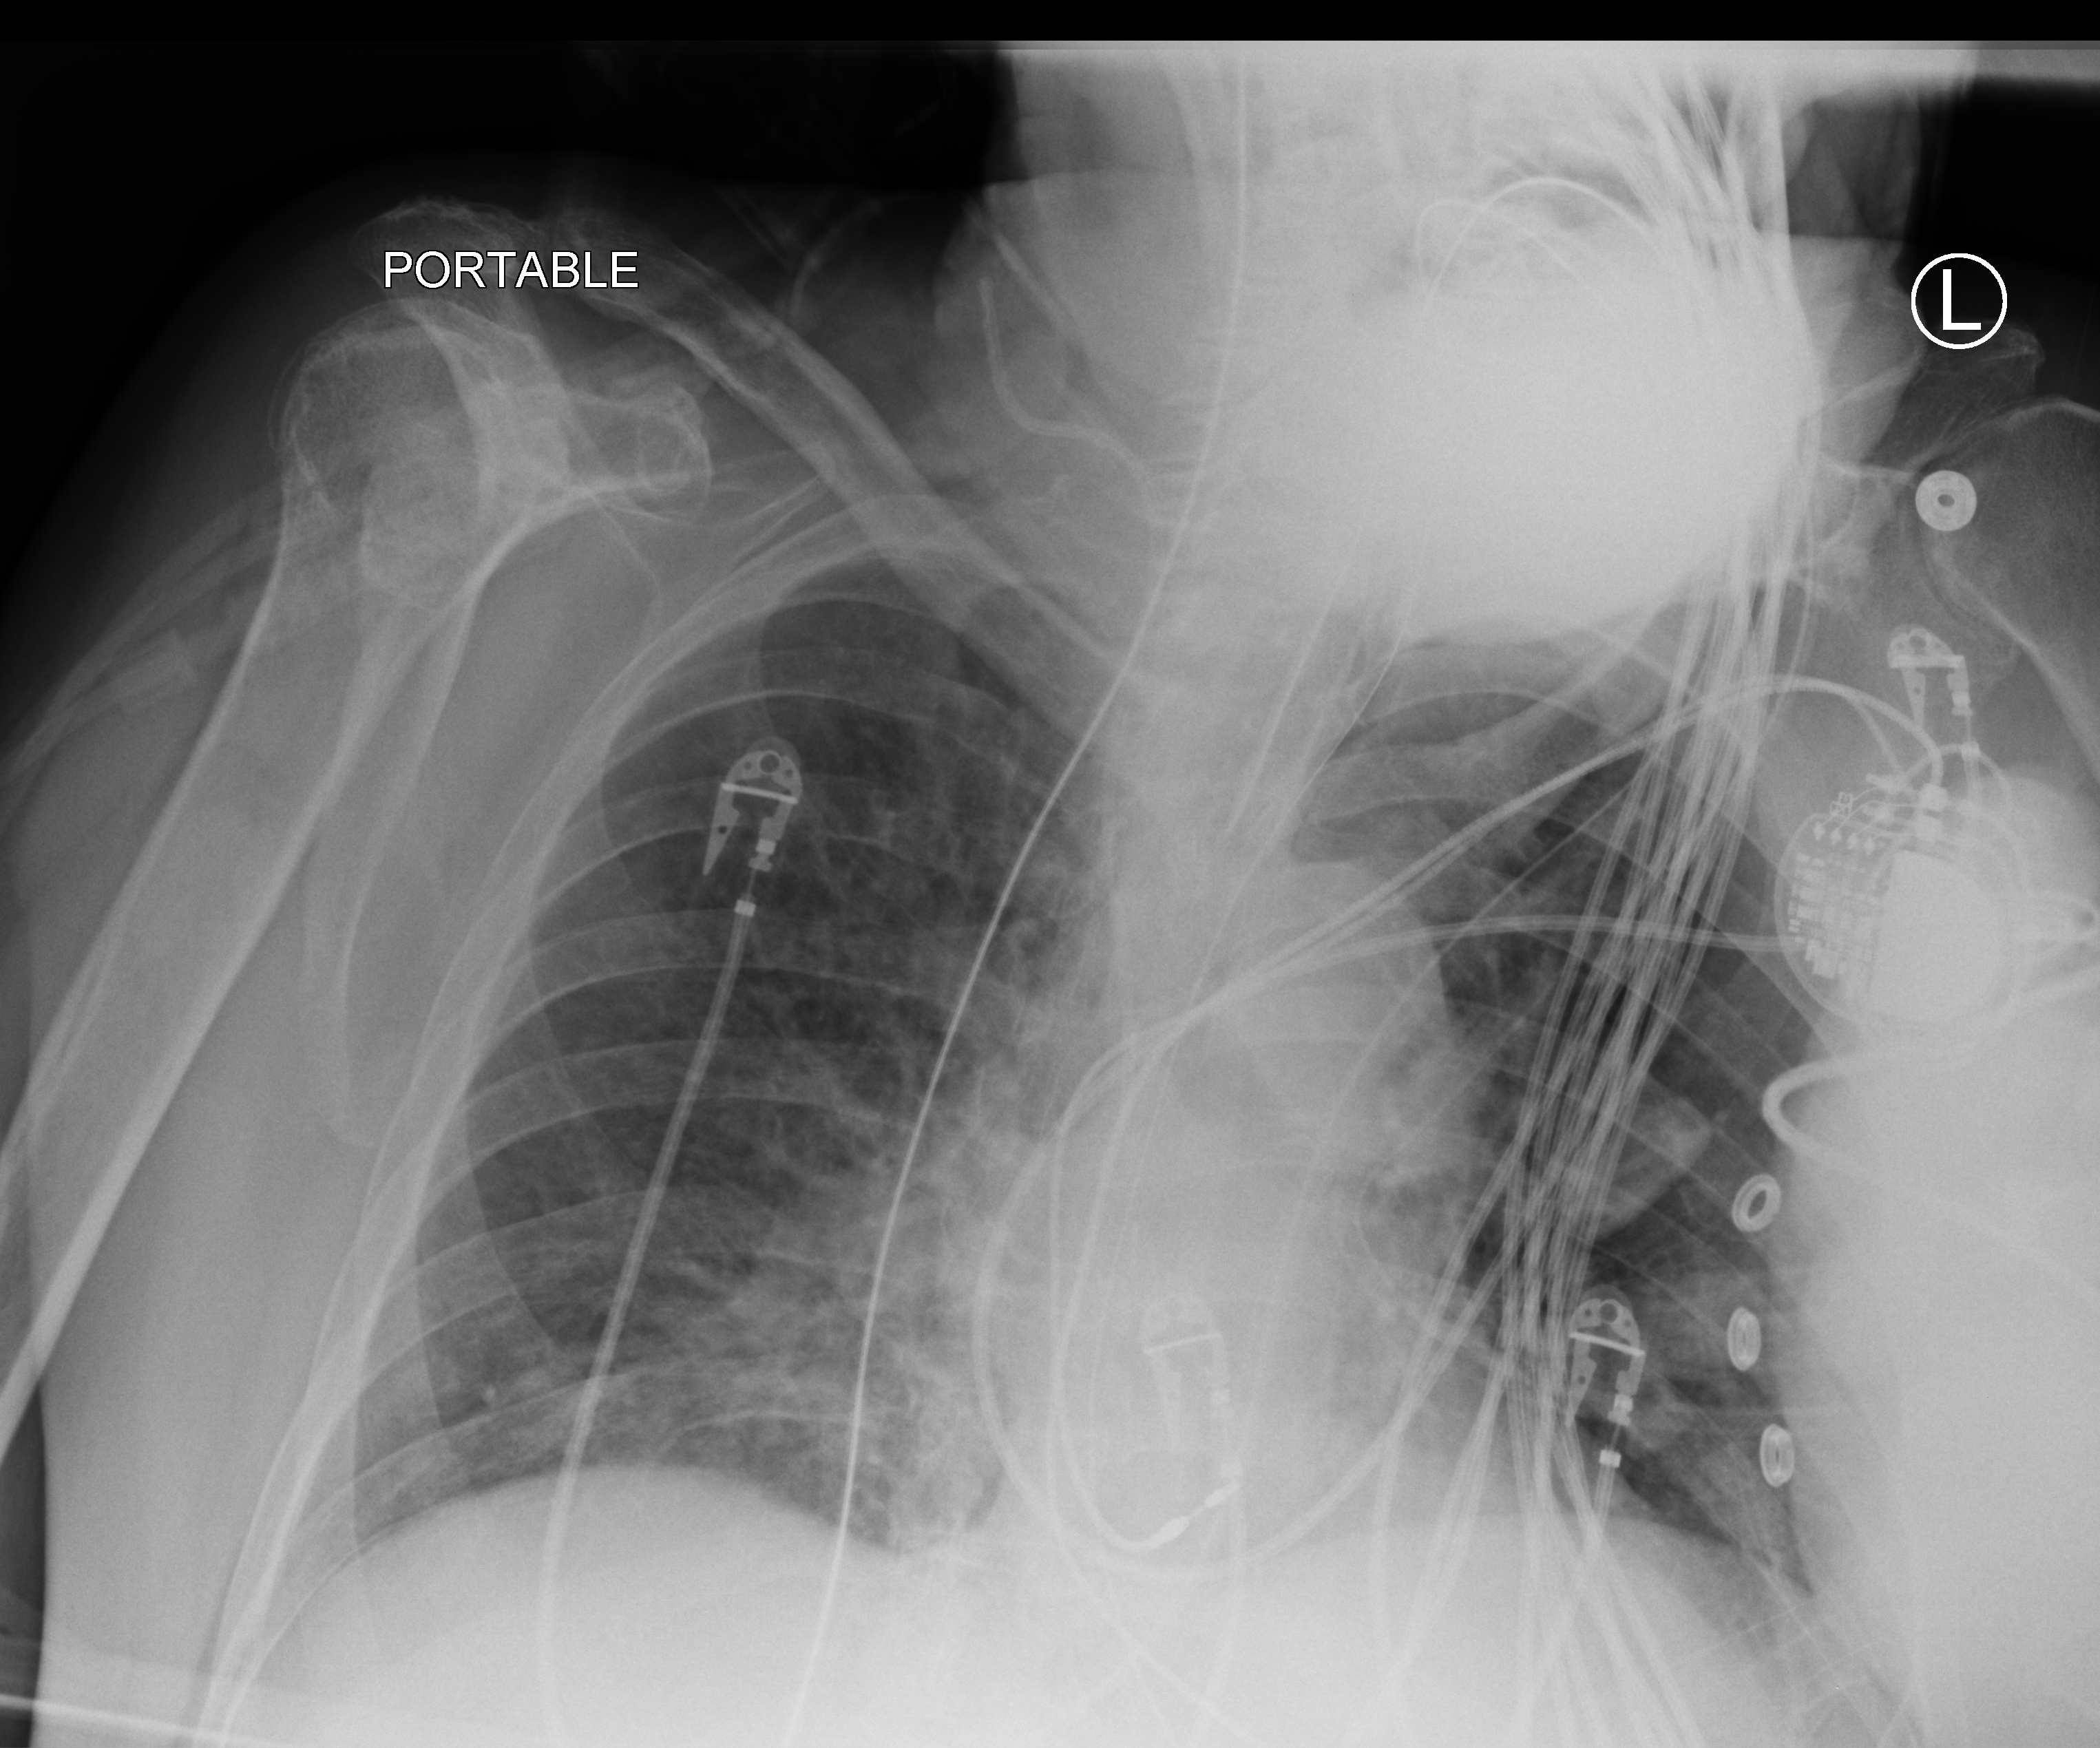
Chest X-ray (portable), anteroposterior (AP) projection. Patient hospitalised with COVID-19; male, aged 60–74 years.
Admission-level facts for this patient (not findings on this image; timing relative to this image not recorded):
- admitted to intensive care during this hospital stay: no